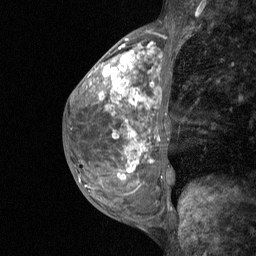
Breast MRI (dynamic contrast-enhanced), one sagittal slice. Slice 26 of 64 in the series (ordered by position). Dynamic contrast-enhanced study with each time point stored as its own series, time point 2 of 3 at this slice position (early post-contrast, ordered by acquisition time). 1.5 T. TE 4.8 ms, TR 27 ms. 2 mm slice thickness. 256 × 256 image matrix, field of view 200 × 200 mm. Patient: female, 36 years. Case-level facts recorded for this patient, not image findings: setting: breast cancer imaged before/during neoadjuvant chemotherapy; receptor status: HR-positive, HER2-negative.
Outlined on this slice (semi-automatically segmented with operator editing):
- analysis volume of interest (the breast-tissue region the enhancement analysis was run in; not a lesion): box from (x=73, y=54) to (x=173, y=210) px
- tumour enhancement mask (voxels above the 90 % enhancement threshold inside the analysis volume of interest): (x=104, y=56)–(x=132, y=87)